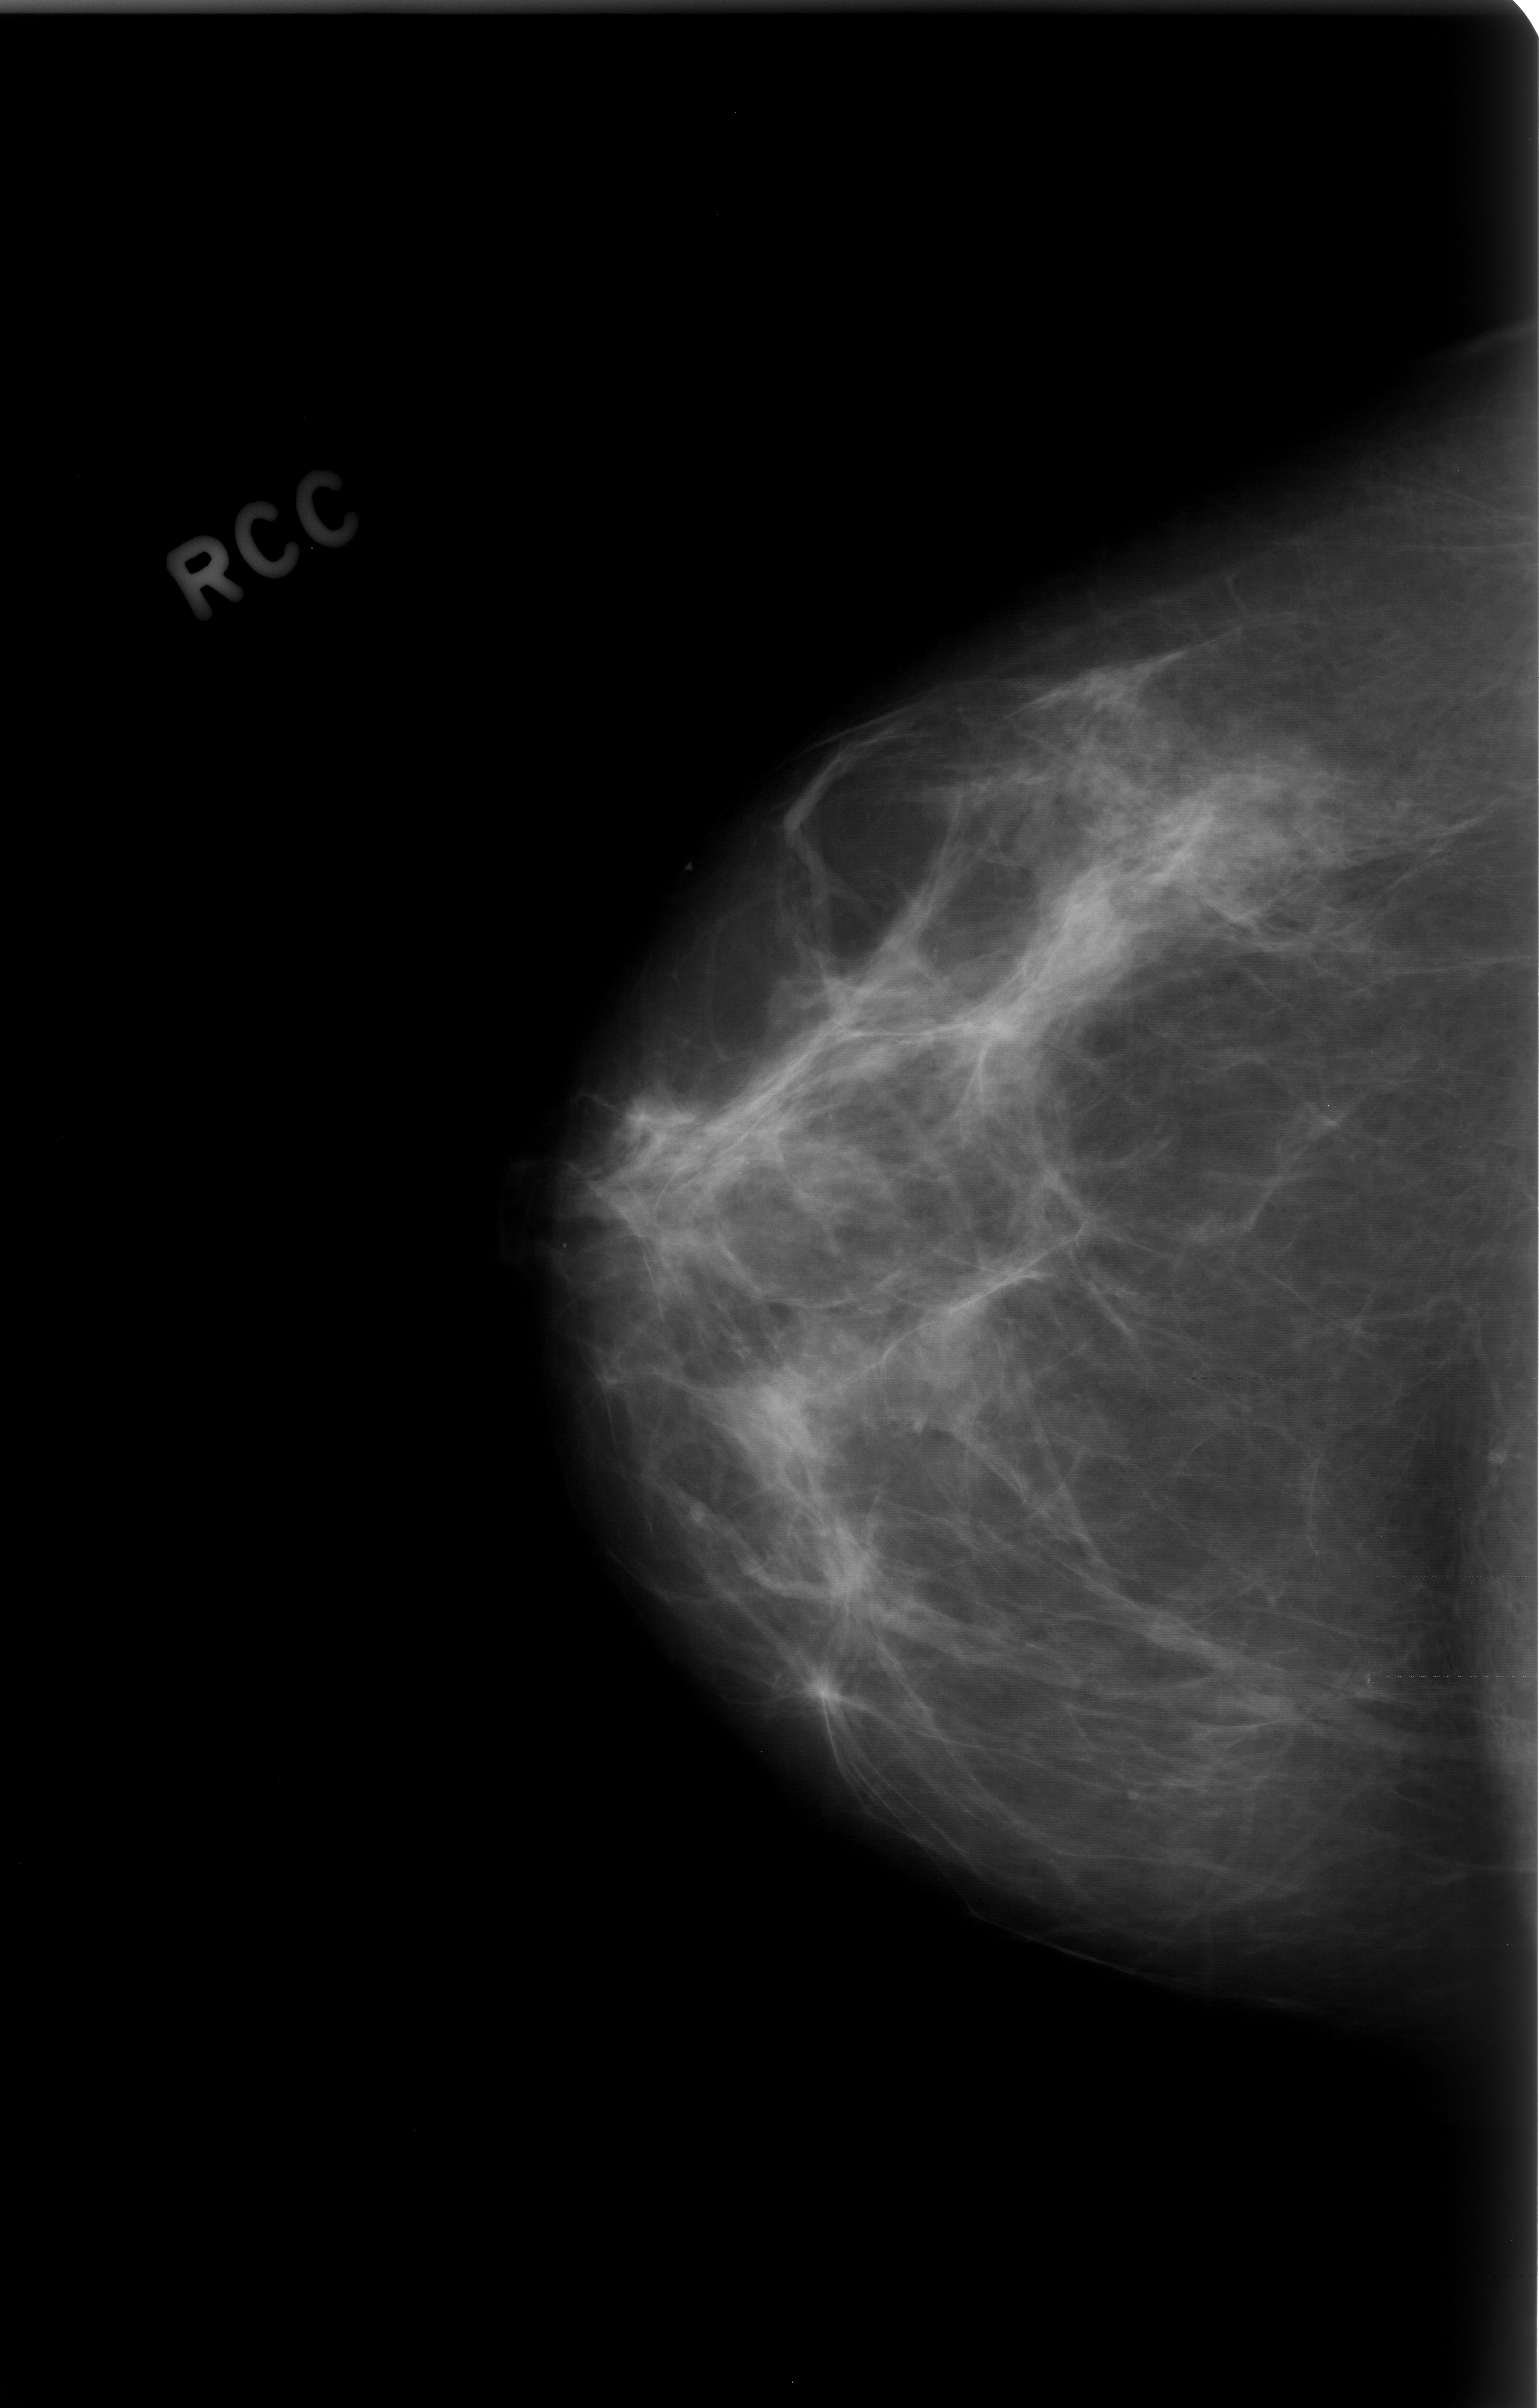
Digitized screen-film mammogram, right breast, craniocaudal (CC) view, breast composition: scattered fibroglandular densities (BI-RADS density category 2 of 4).
Finding: calcifications, morphology amorphous, distribution clustered; BI-RADS assessment category 4; pathology (as recorded): benign.